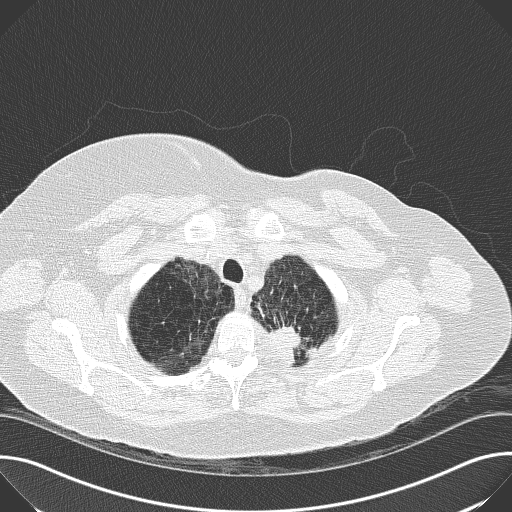
Low-dose screening chest CT, one axial slice; slice 149 of 169 in the series (ordered by position); reconstruction kernel B50f; 120 kVp; lung window (W 1500 / L -600 HU); 2 mm slice thickness; 512 × 512 image matrix, field of view 380 × 380 mm.
Structures marked on this image (expert manual segmentation):
- lesion 1 (tumor, upper lobe of left lung): box from (x=267, y=326) to (x=318, y=367) px